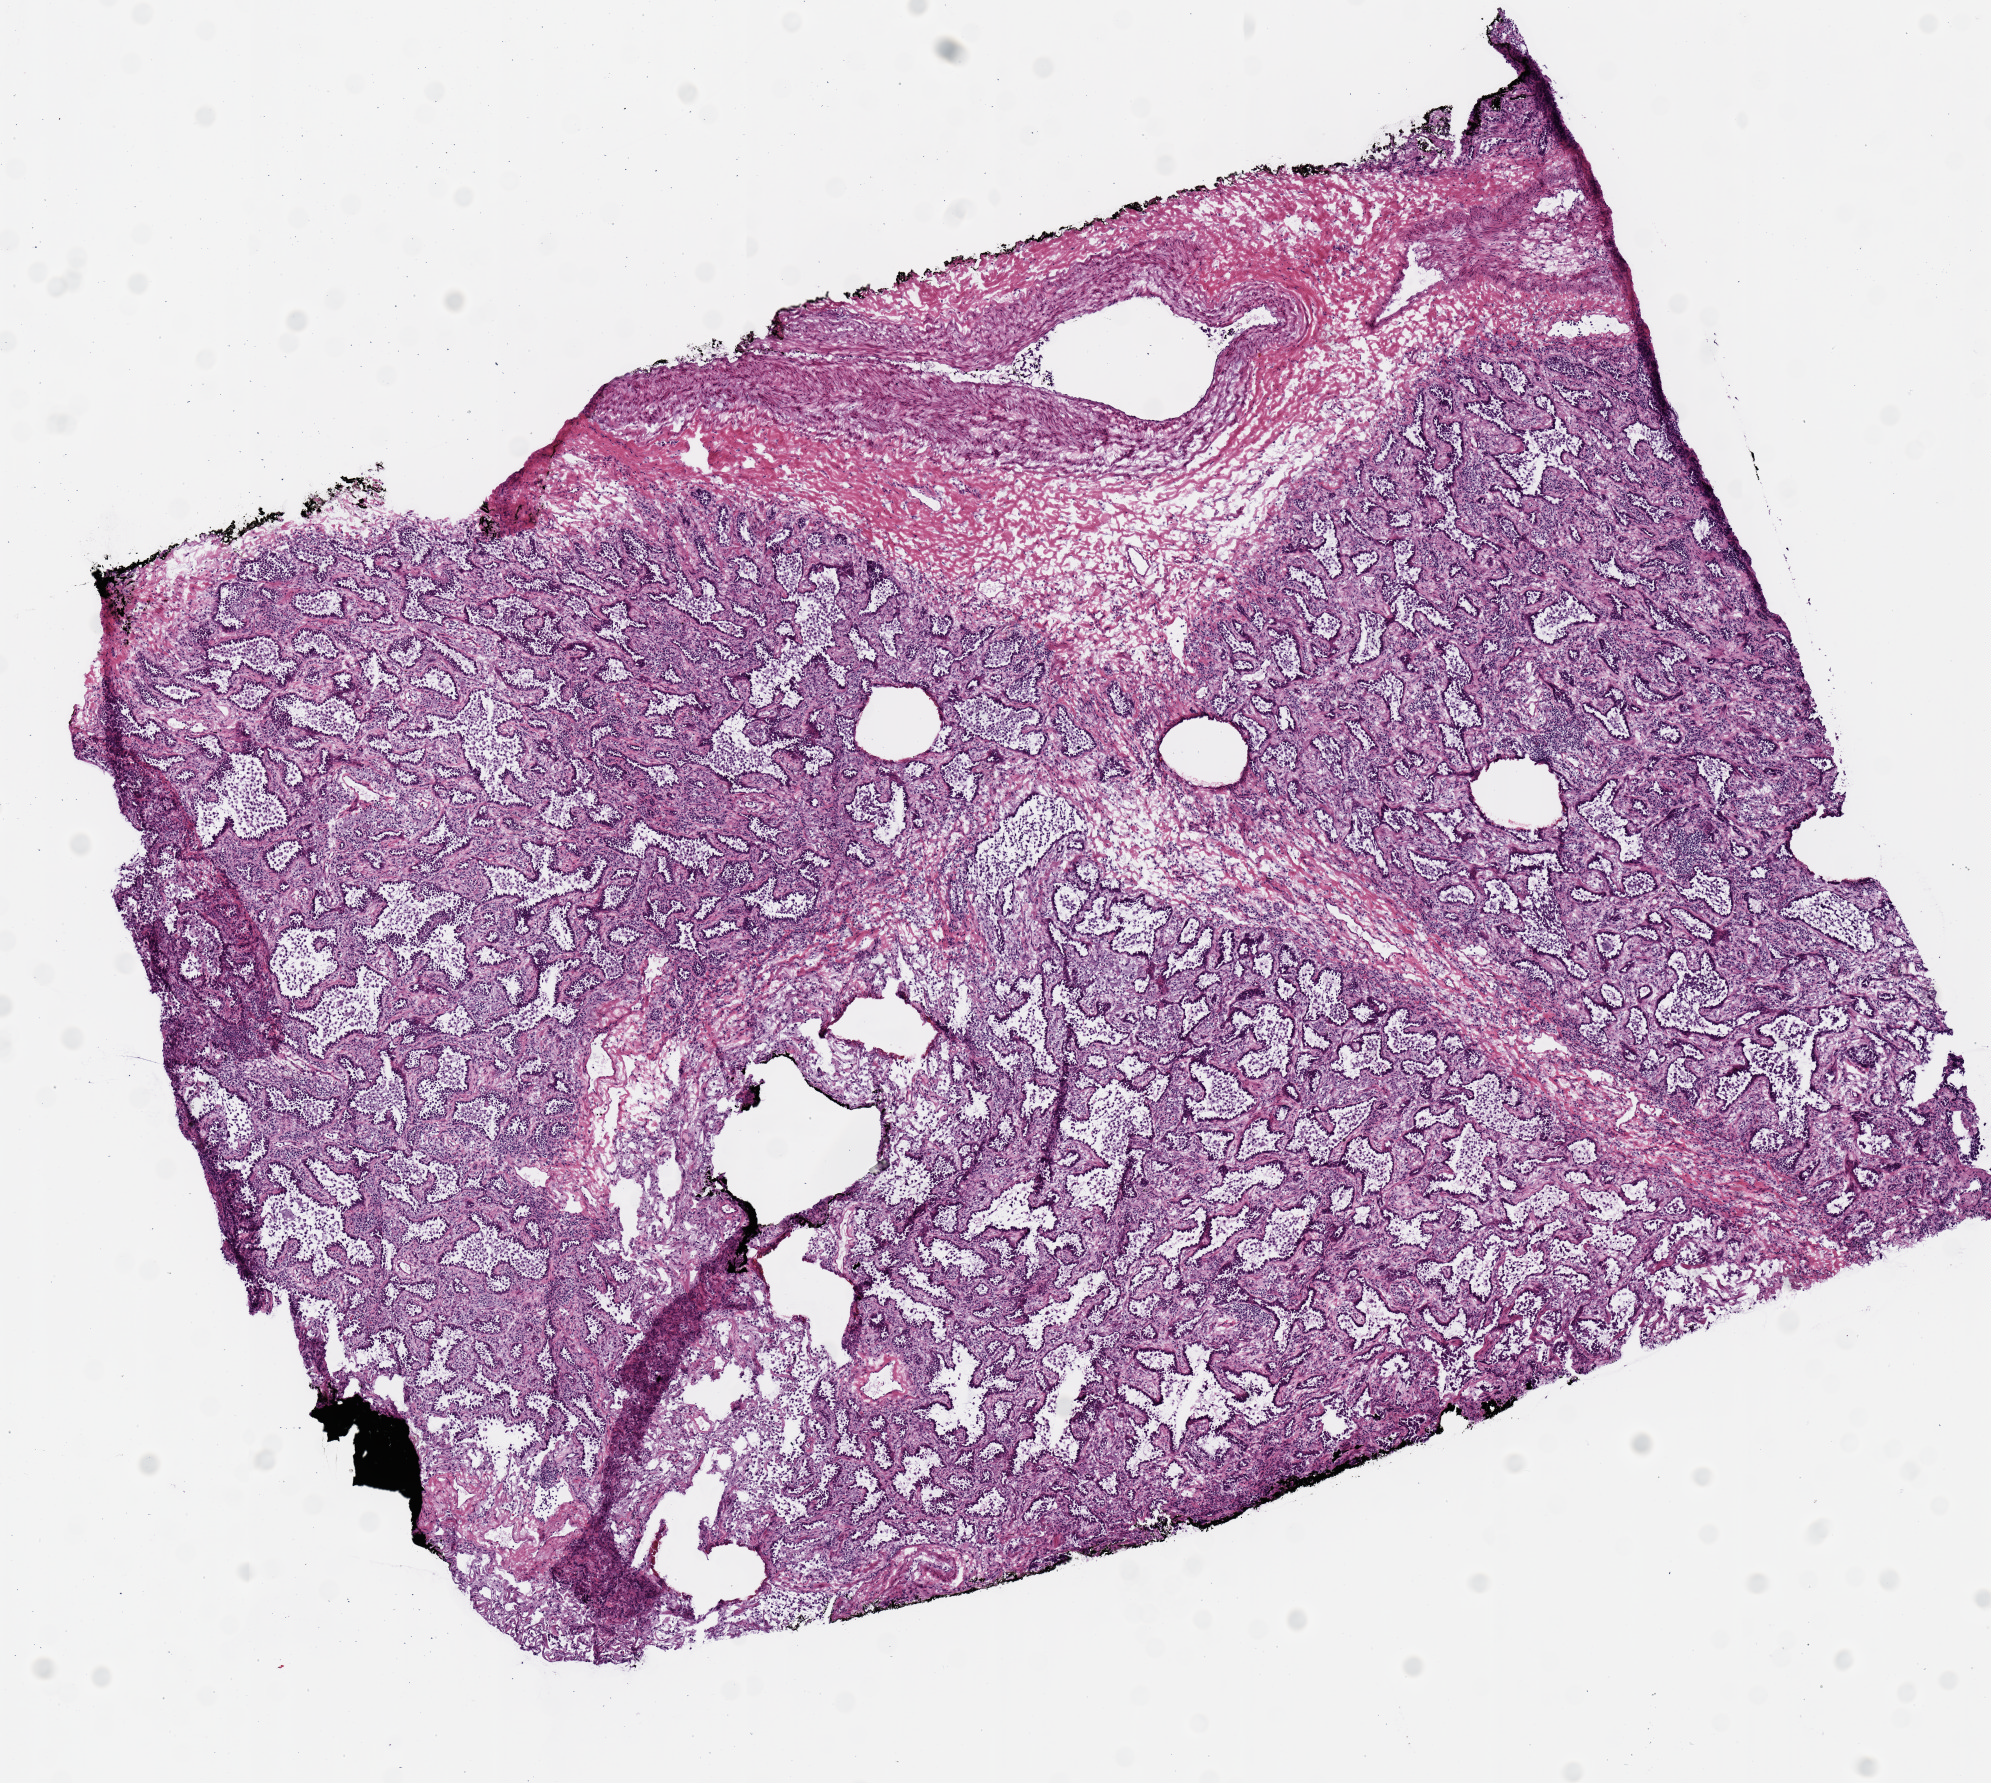
Whole-slide histology image, Hematoxylin and eosin (H&E) stained, whole scanned area (about 7.9 x 7.0 mm) shown as a low-resolution overview. Frozen section from the top of the tissue portion. Sample: primary tumour, lung. Male patient; age at initial diagnosis 56 years. Pathologist review of this section (percent, as recorded): tumour cells 0%, tumour nuclei 65%, normal cells 0%, stromal cells 0%, necrosis 0%.
* diagnosis: Adenocarcinoma, NOS (upper lobe, lung)
* laterality: right
* AJCC pathologic stage: IA (7th edition)